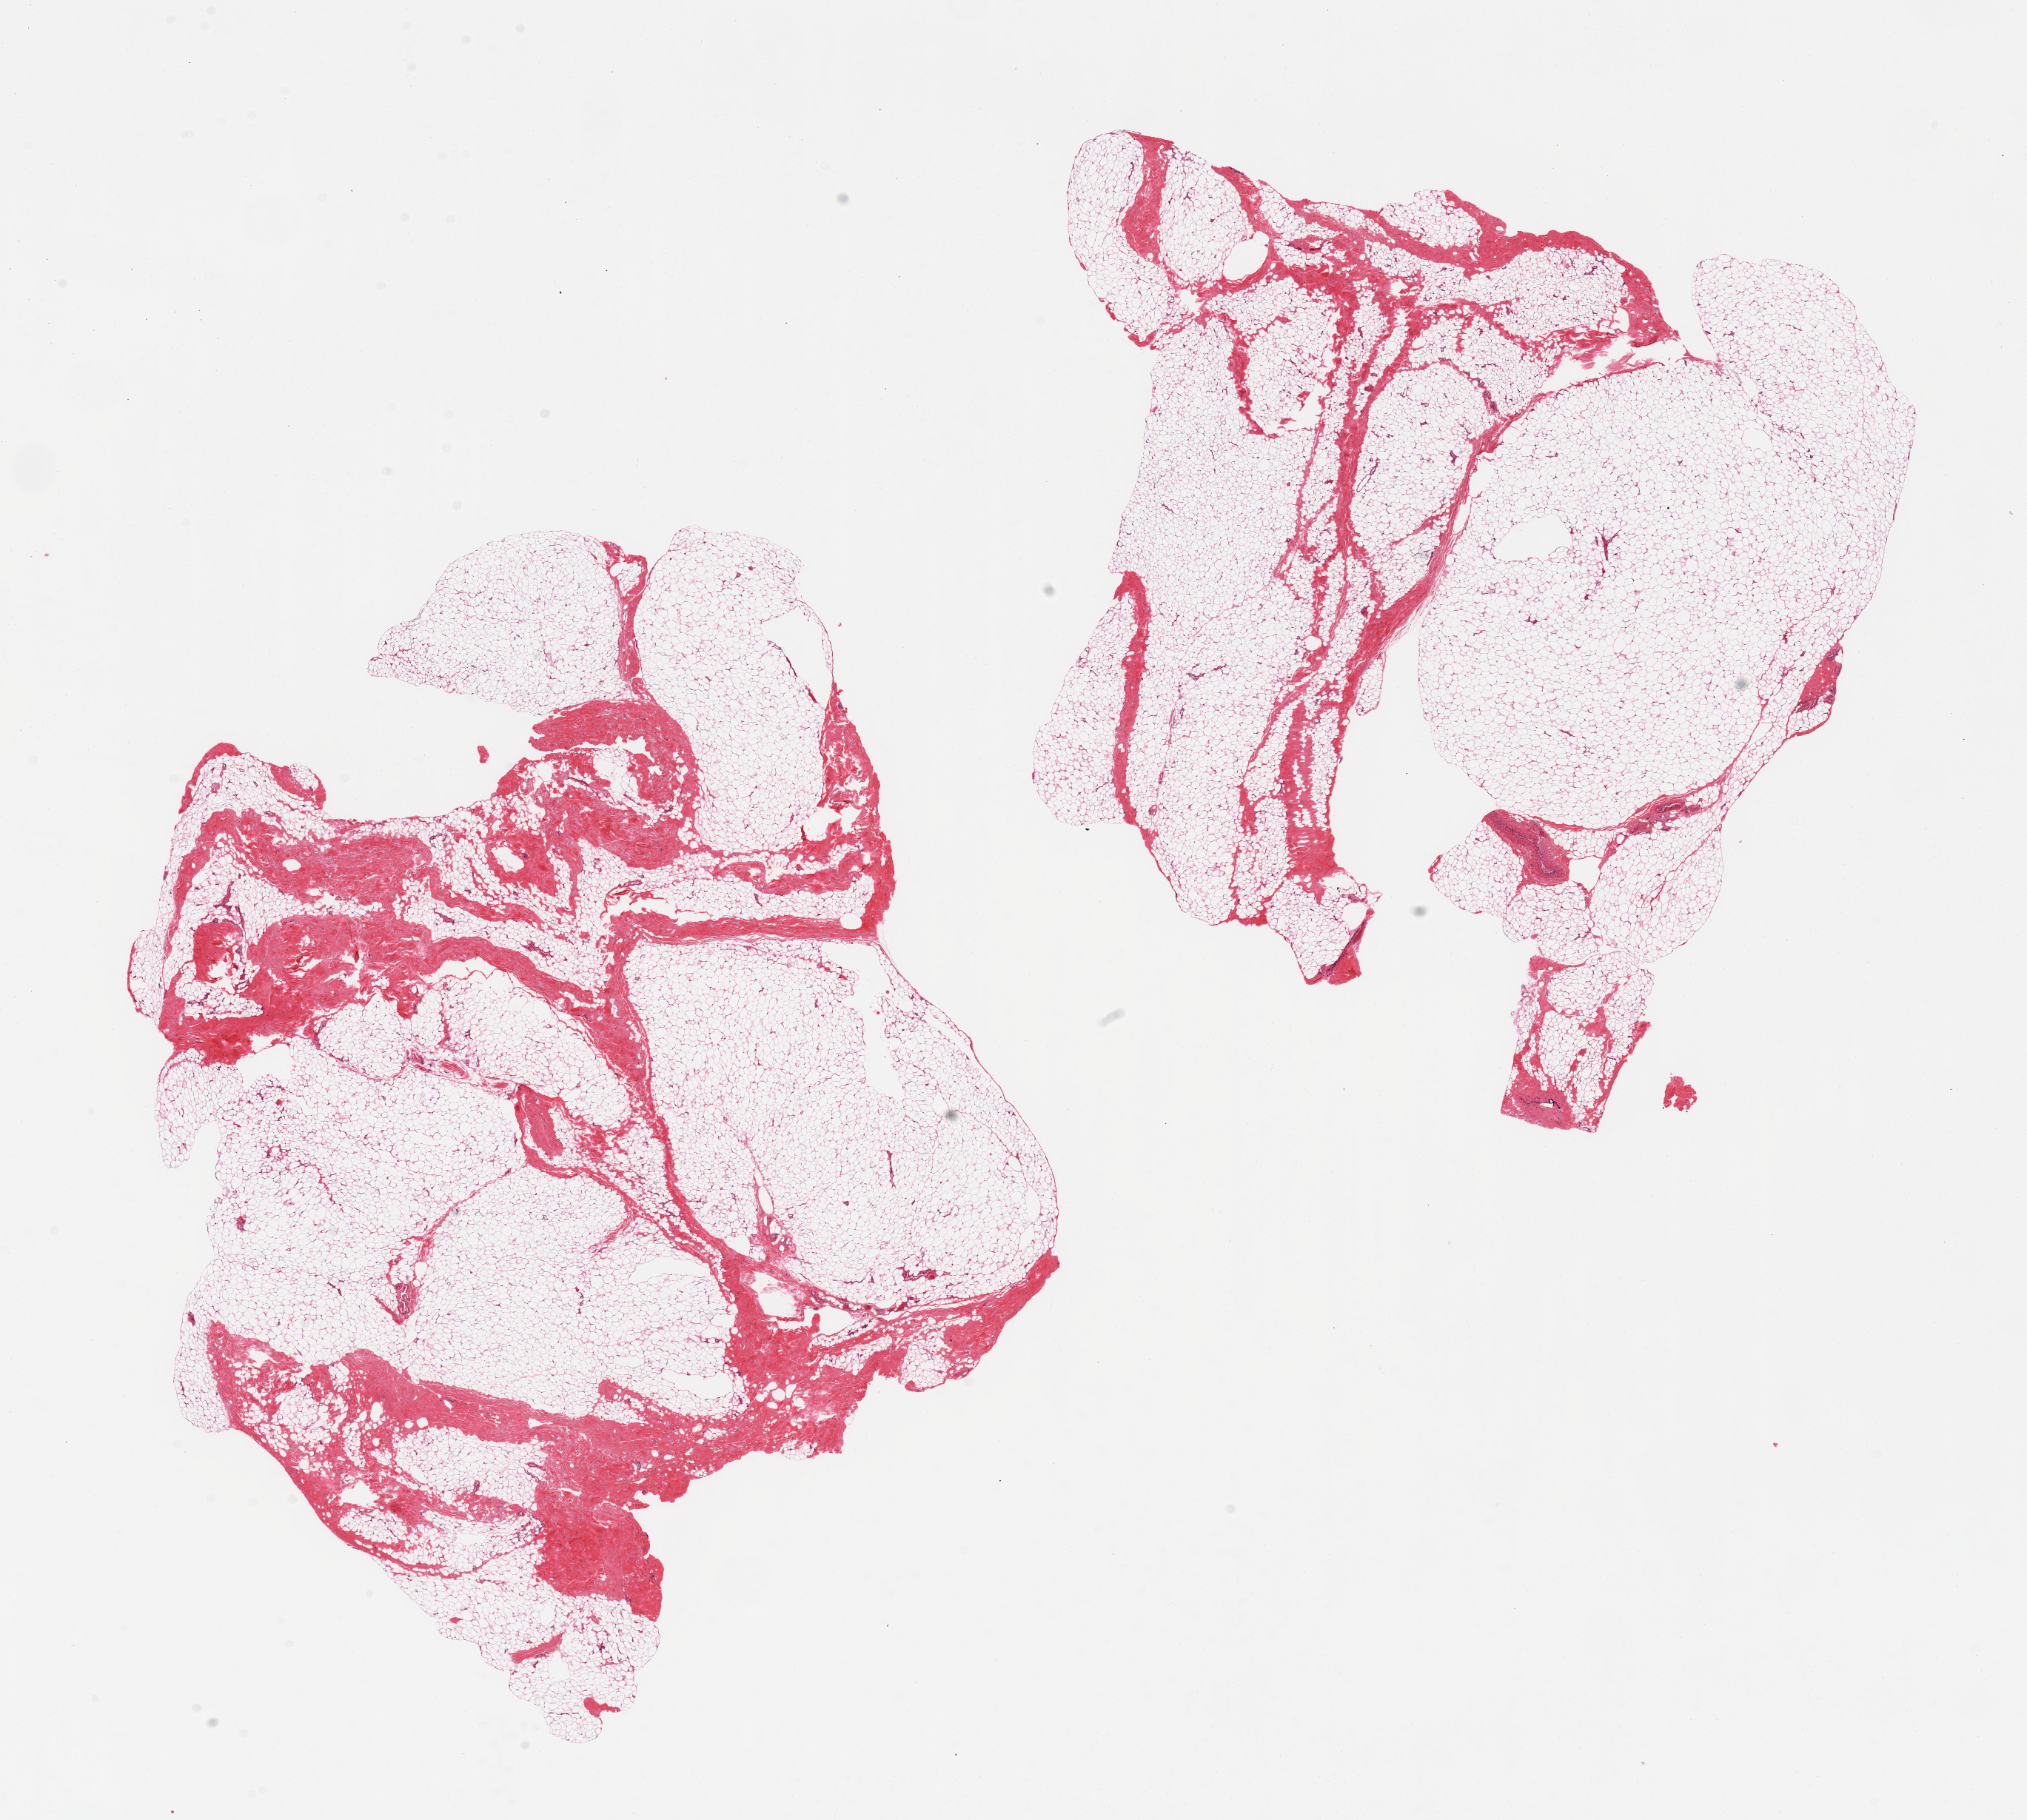
Whole-slide image, H&E stain, brightfield — whole scanned area (about 21.7 x 19.4 mm) shown as a low-resolution overview; PAXgene-fixed, paraffin-embedded tissue; target tissue: breast; tissue donor sample. Male donor.
Reviewer comment on this tissue sample: 2 pieces, fibroadipose tissue; no ductal elements noted.